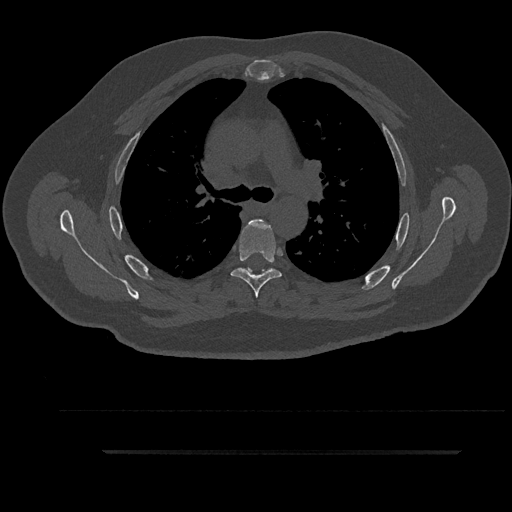
CT including the spine, one axial slice; position 627 of 797 along the scan axis; 120 kVp; bone window (W 1800 / L 400 HU); 512 × 512 image matrix. Patient: male, 63 years. Case-level facts recorded for this patient, not image findings: primary cancer: renal; vertebrae with lytic lesions (as recorded): T8.
Outlined on this slice (semi-automatically segmented with operator editing):
- T4 vertebra: box from (x=248, y=219) to (x=263, y=225) px
- T5 vertebra: (x=231, y=220)–(x=282, y=298)
- T6 vertebra: (x=243, y=268)–(x=273, y=276)